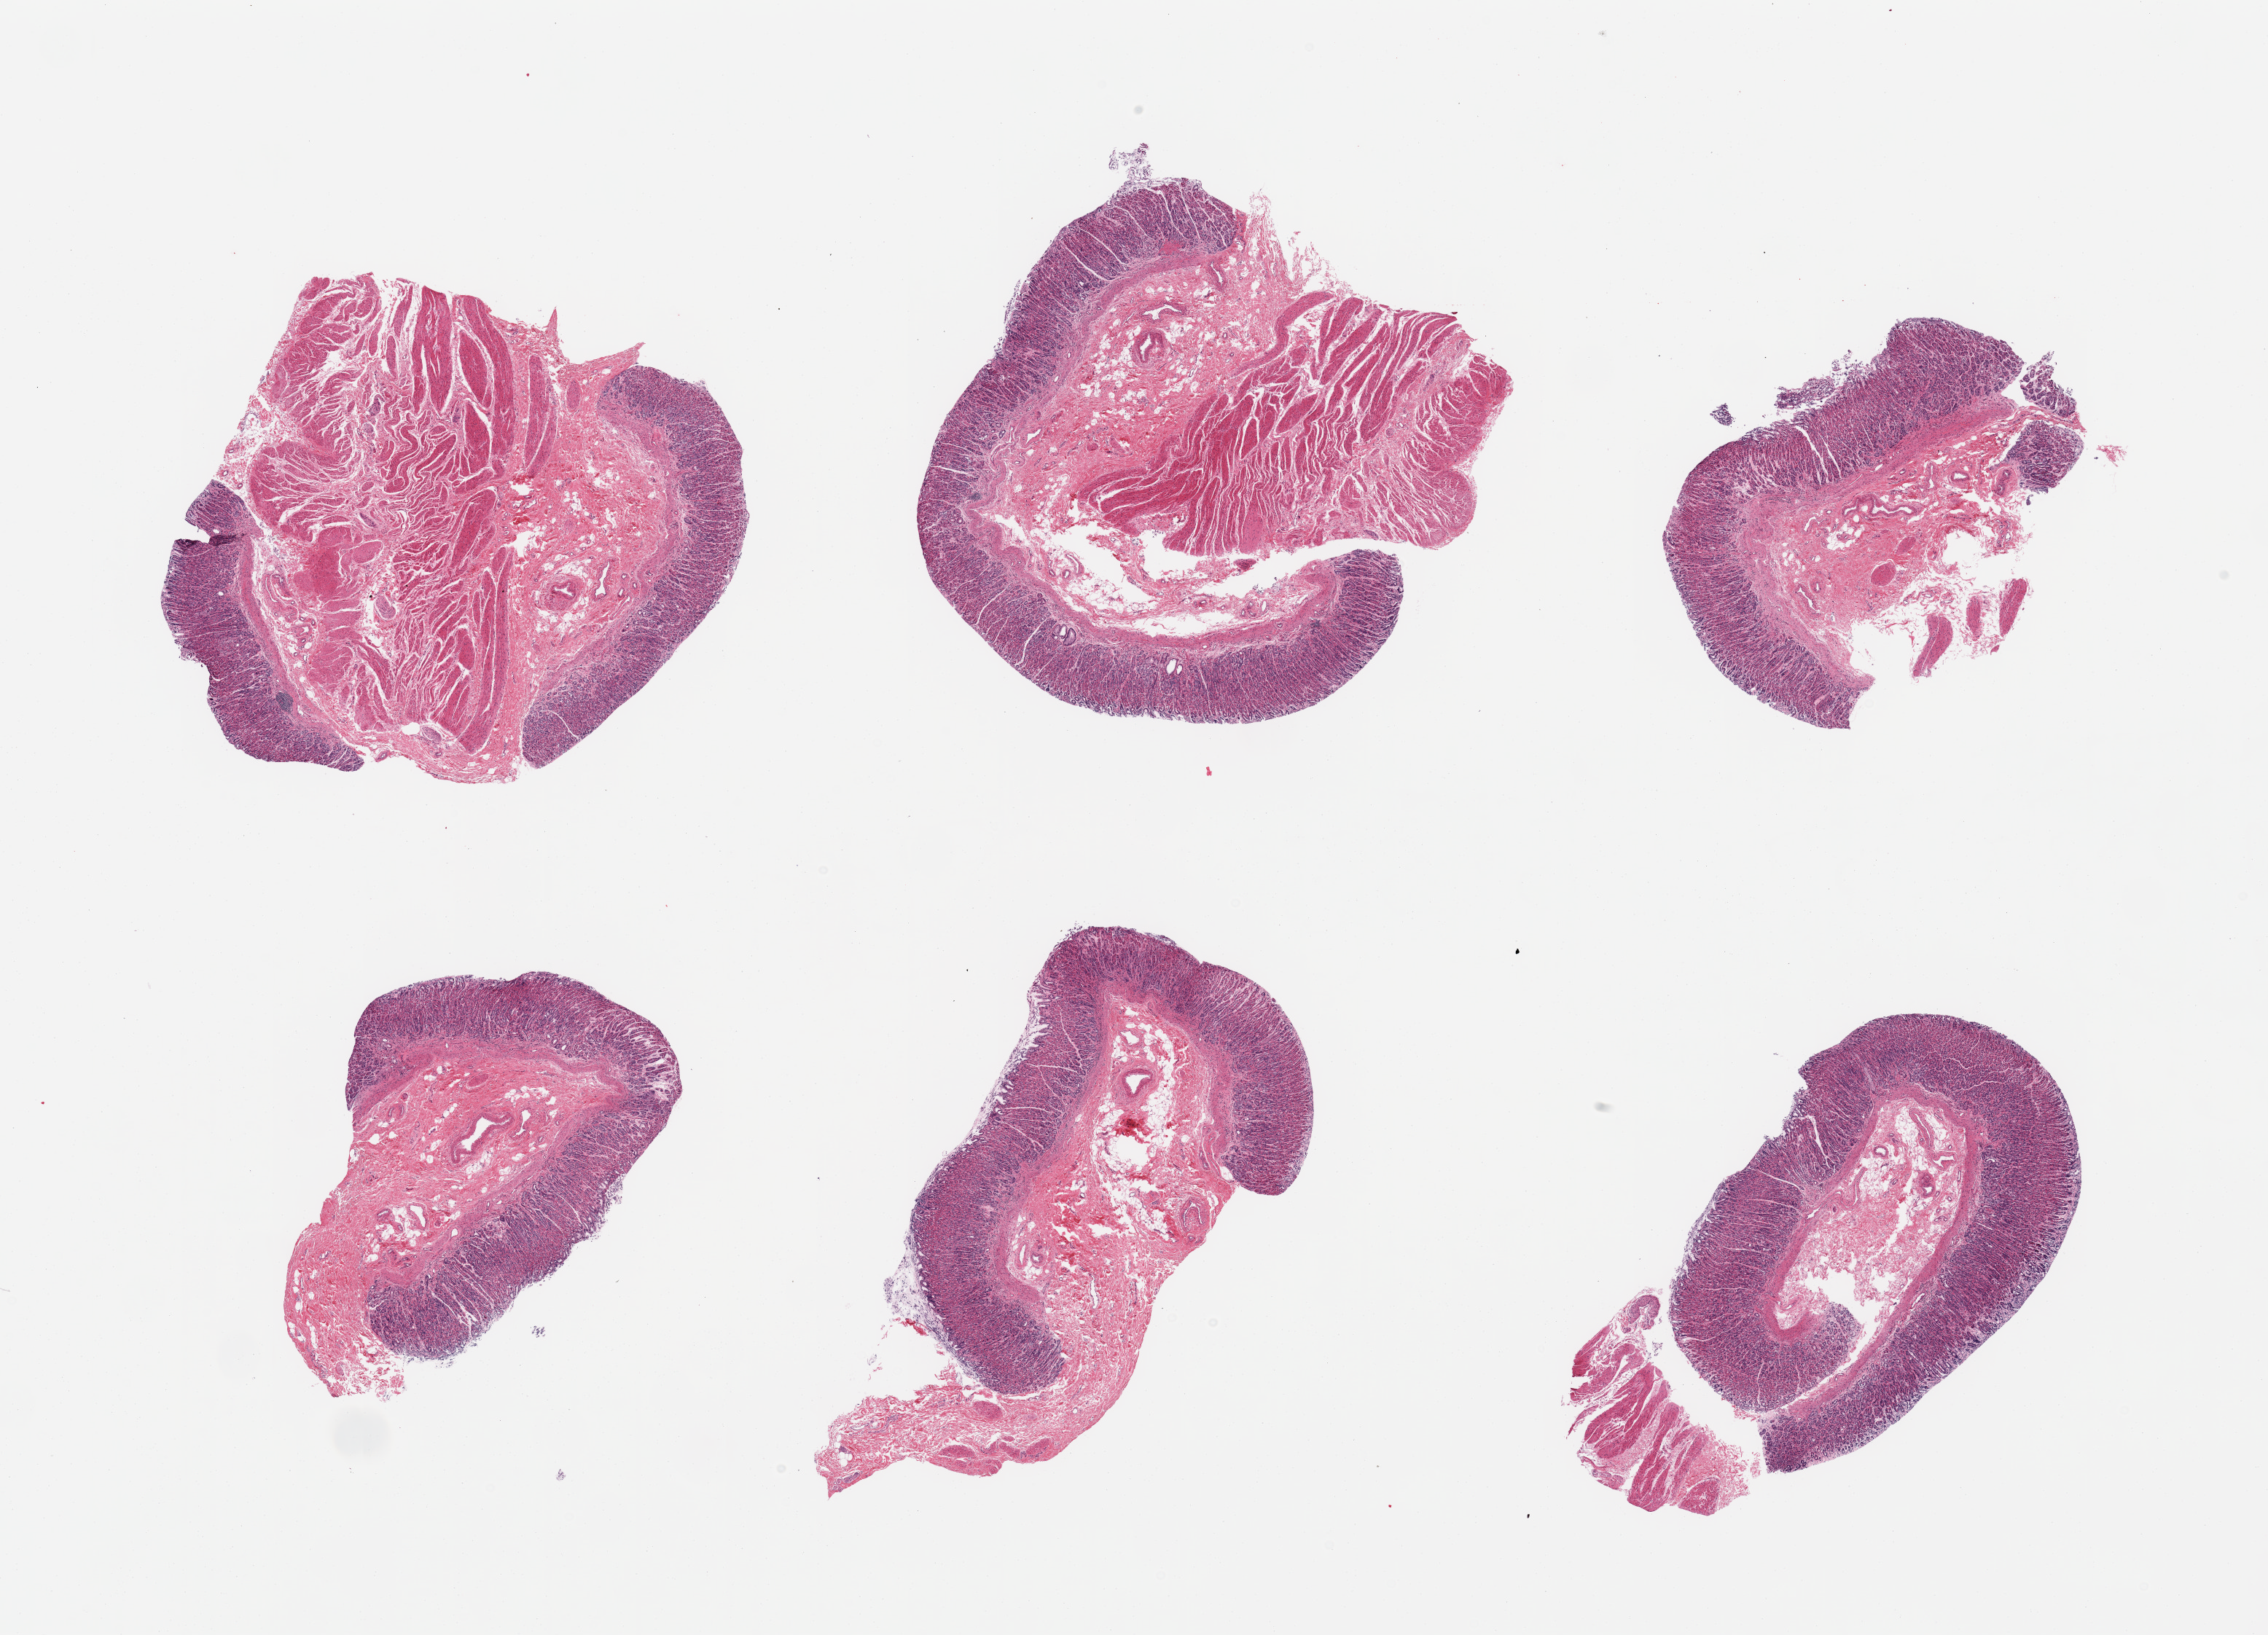
Whole-slide image, haematoxylin and eosin stain — whole scanned area (about 24.6 x 17.7 mm) shown as a low-resolution overview; PAXgene-fixed paraffin-embedded (PFPE) section; sampled site (target tissue): gastroesophageal junction; donor tissue sample. Male donor.
Review note (as recorded): 6 pieces; variable representation of gastric mucosa (not target) and muscularis.